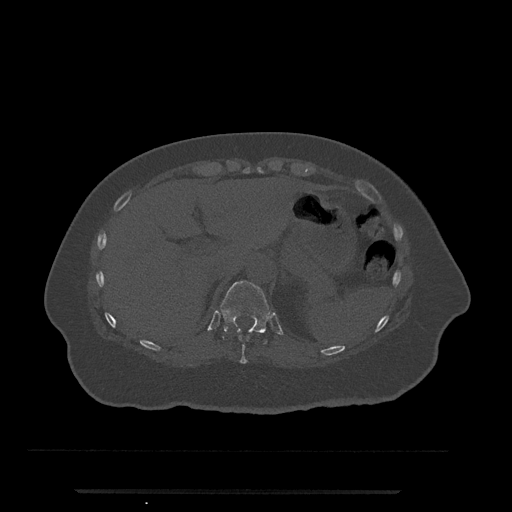
CT including the spine, one axial slice. Slice 248 of 797 in the series (ordered by position). Reconstruction kernel Br40s/3. Bone window (W 1800 / L 400 HU). 0.5 mm slice thickness. 512 × 512 image matrix. Patient: female, 51 years. From the clinical record (not read from this slice): primary cancer: neuro; vertebrae with lytic lesions (as recorded): T8.
Structures marked on this image (semi-automatic segmentation, software-assisted and operator-edited):
- T10 vertebra: box from (x=239, y=338) to (x=249, y=364) px
- T11 vertebra: (x=221, y=281)–(x=271, y=344)